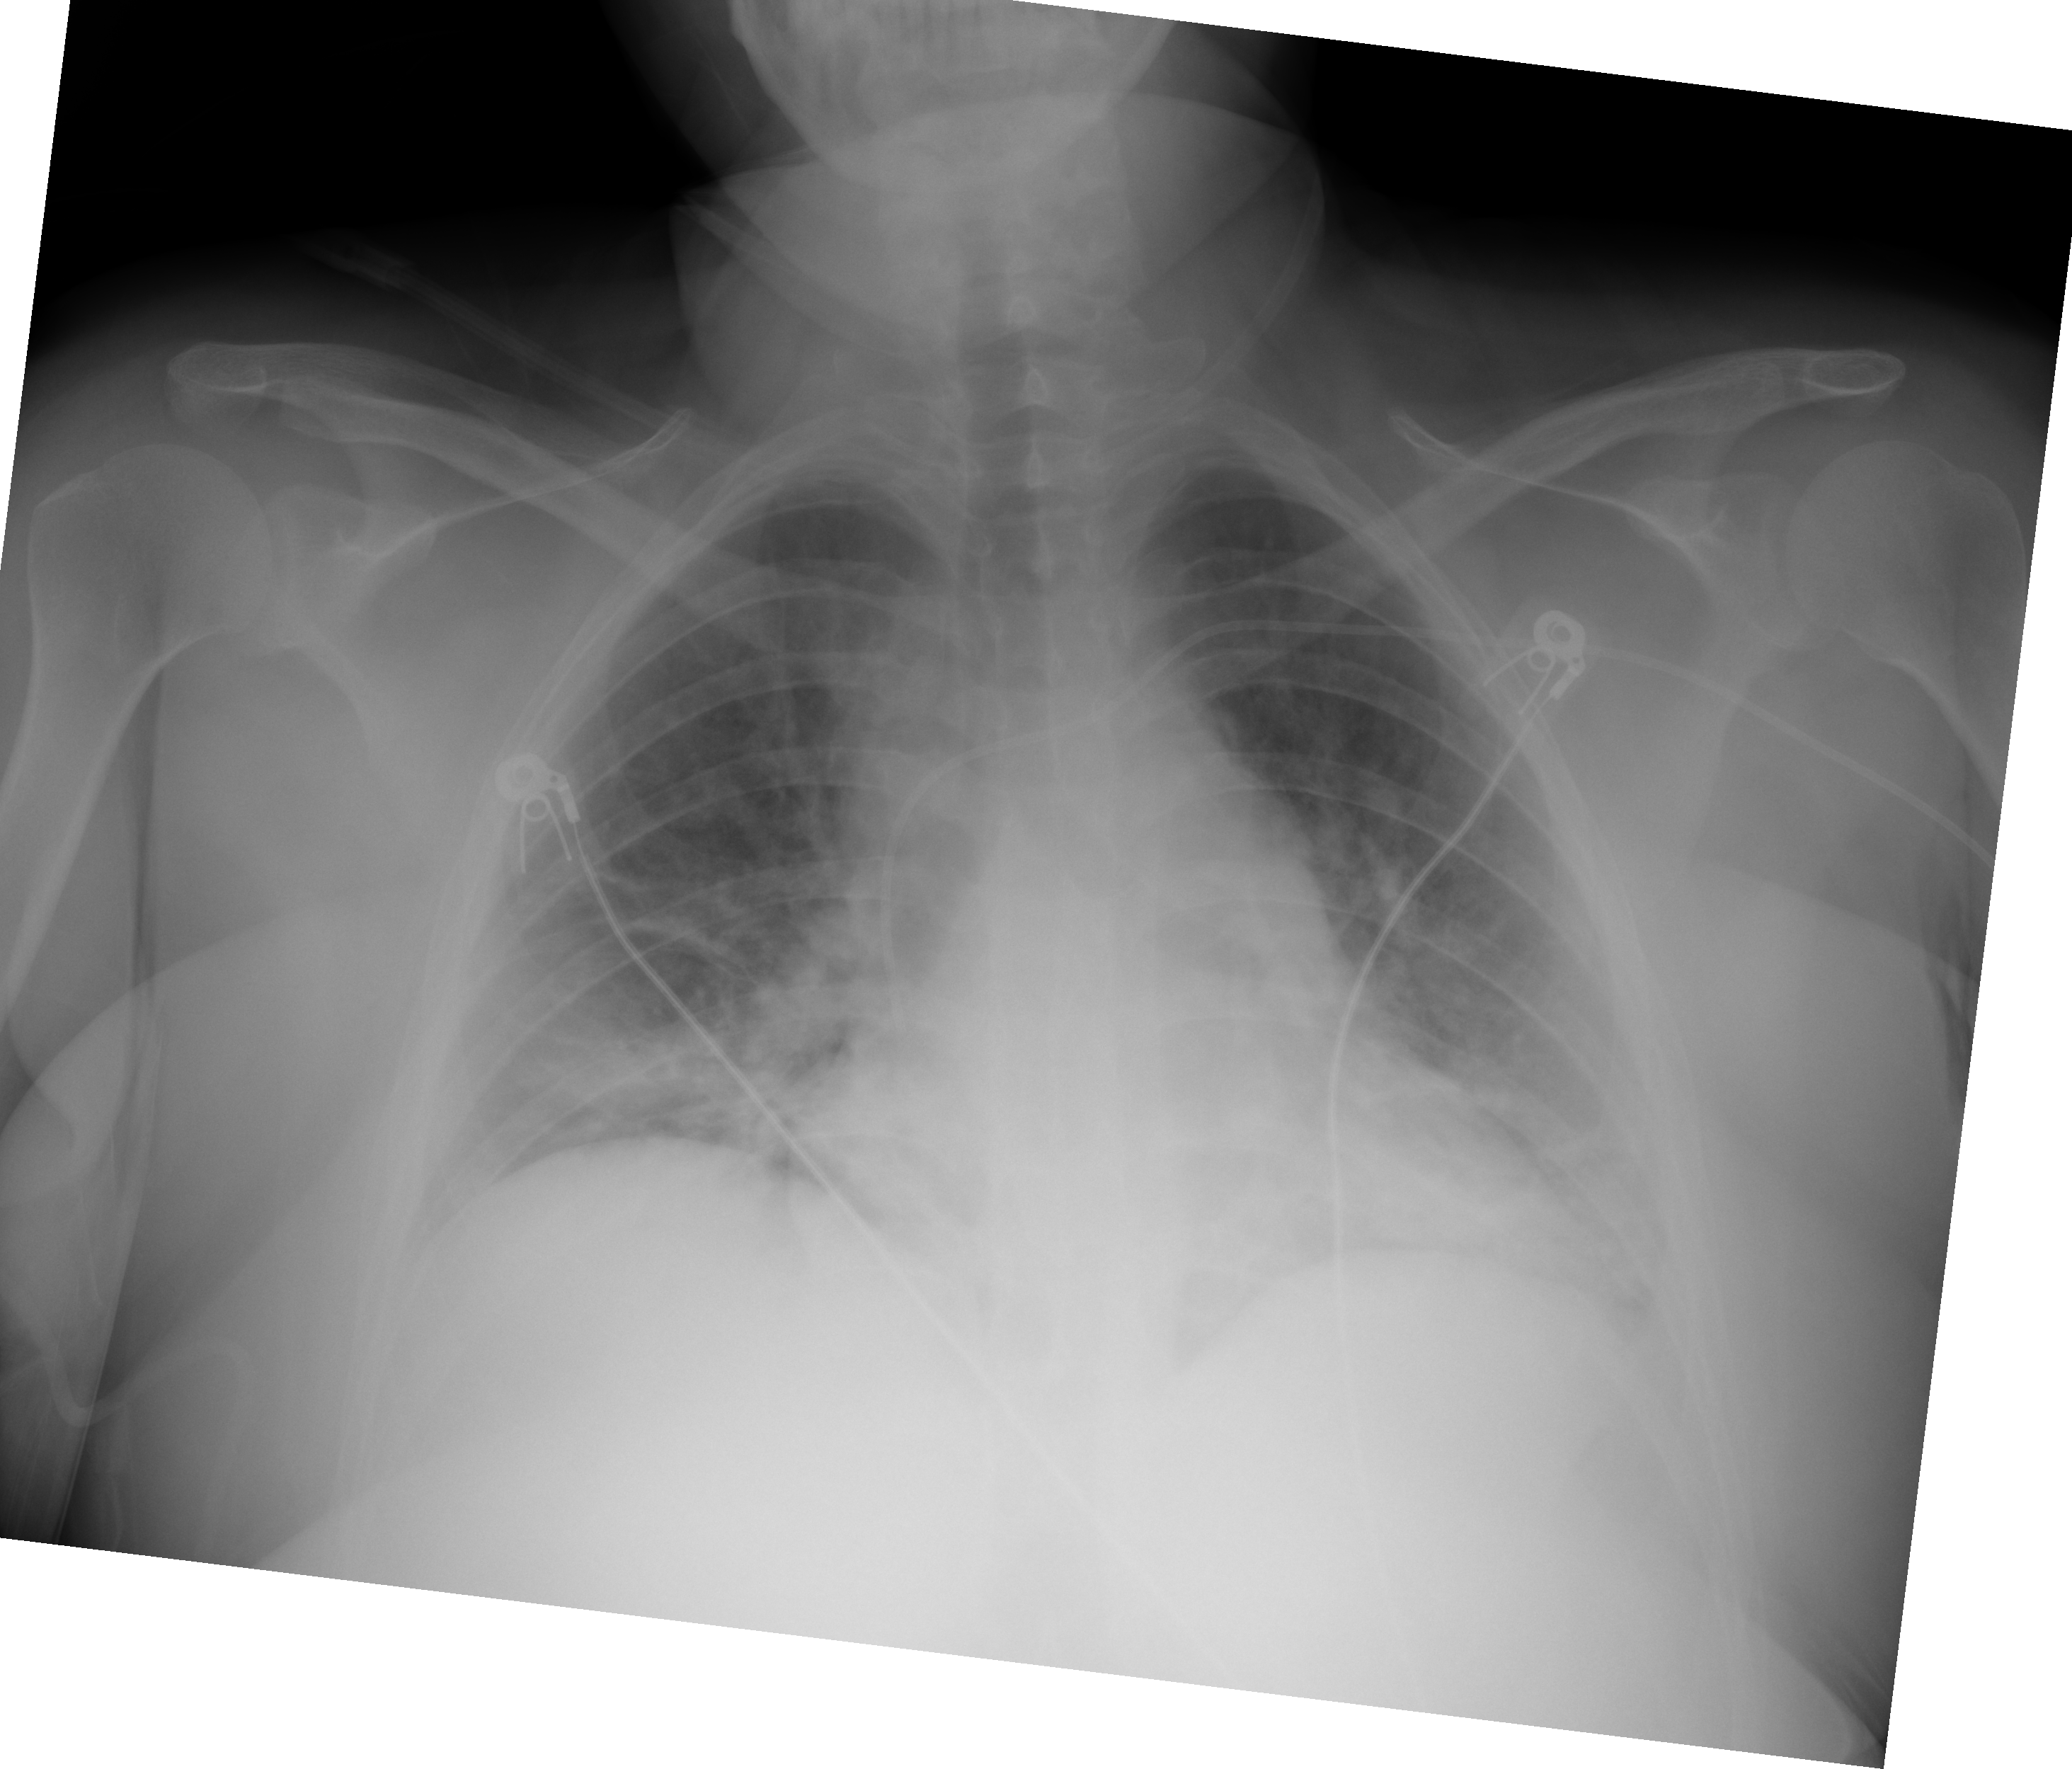
Chest X-ray (portable), AP projection. Female patient, age 29 years; imaged 0 days after the COVID-19 diagnosis.
Radiologist key findings (as recorded): The lungs are hypoinflated with worsening bibasilar opacities.